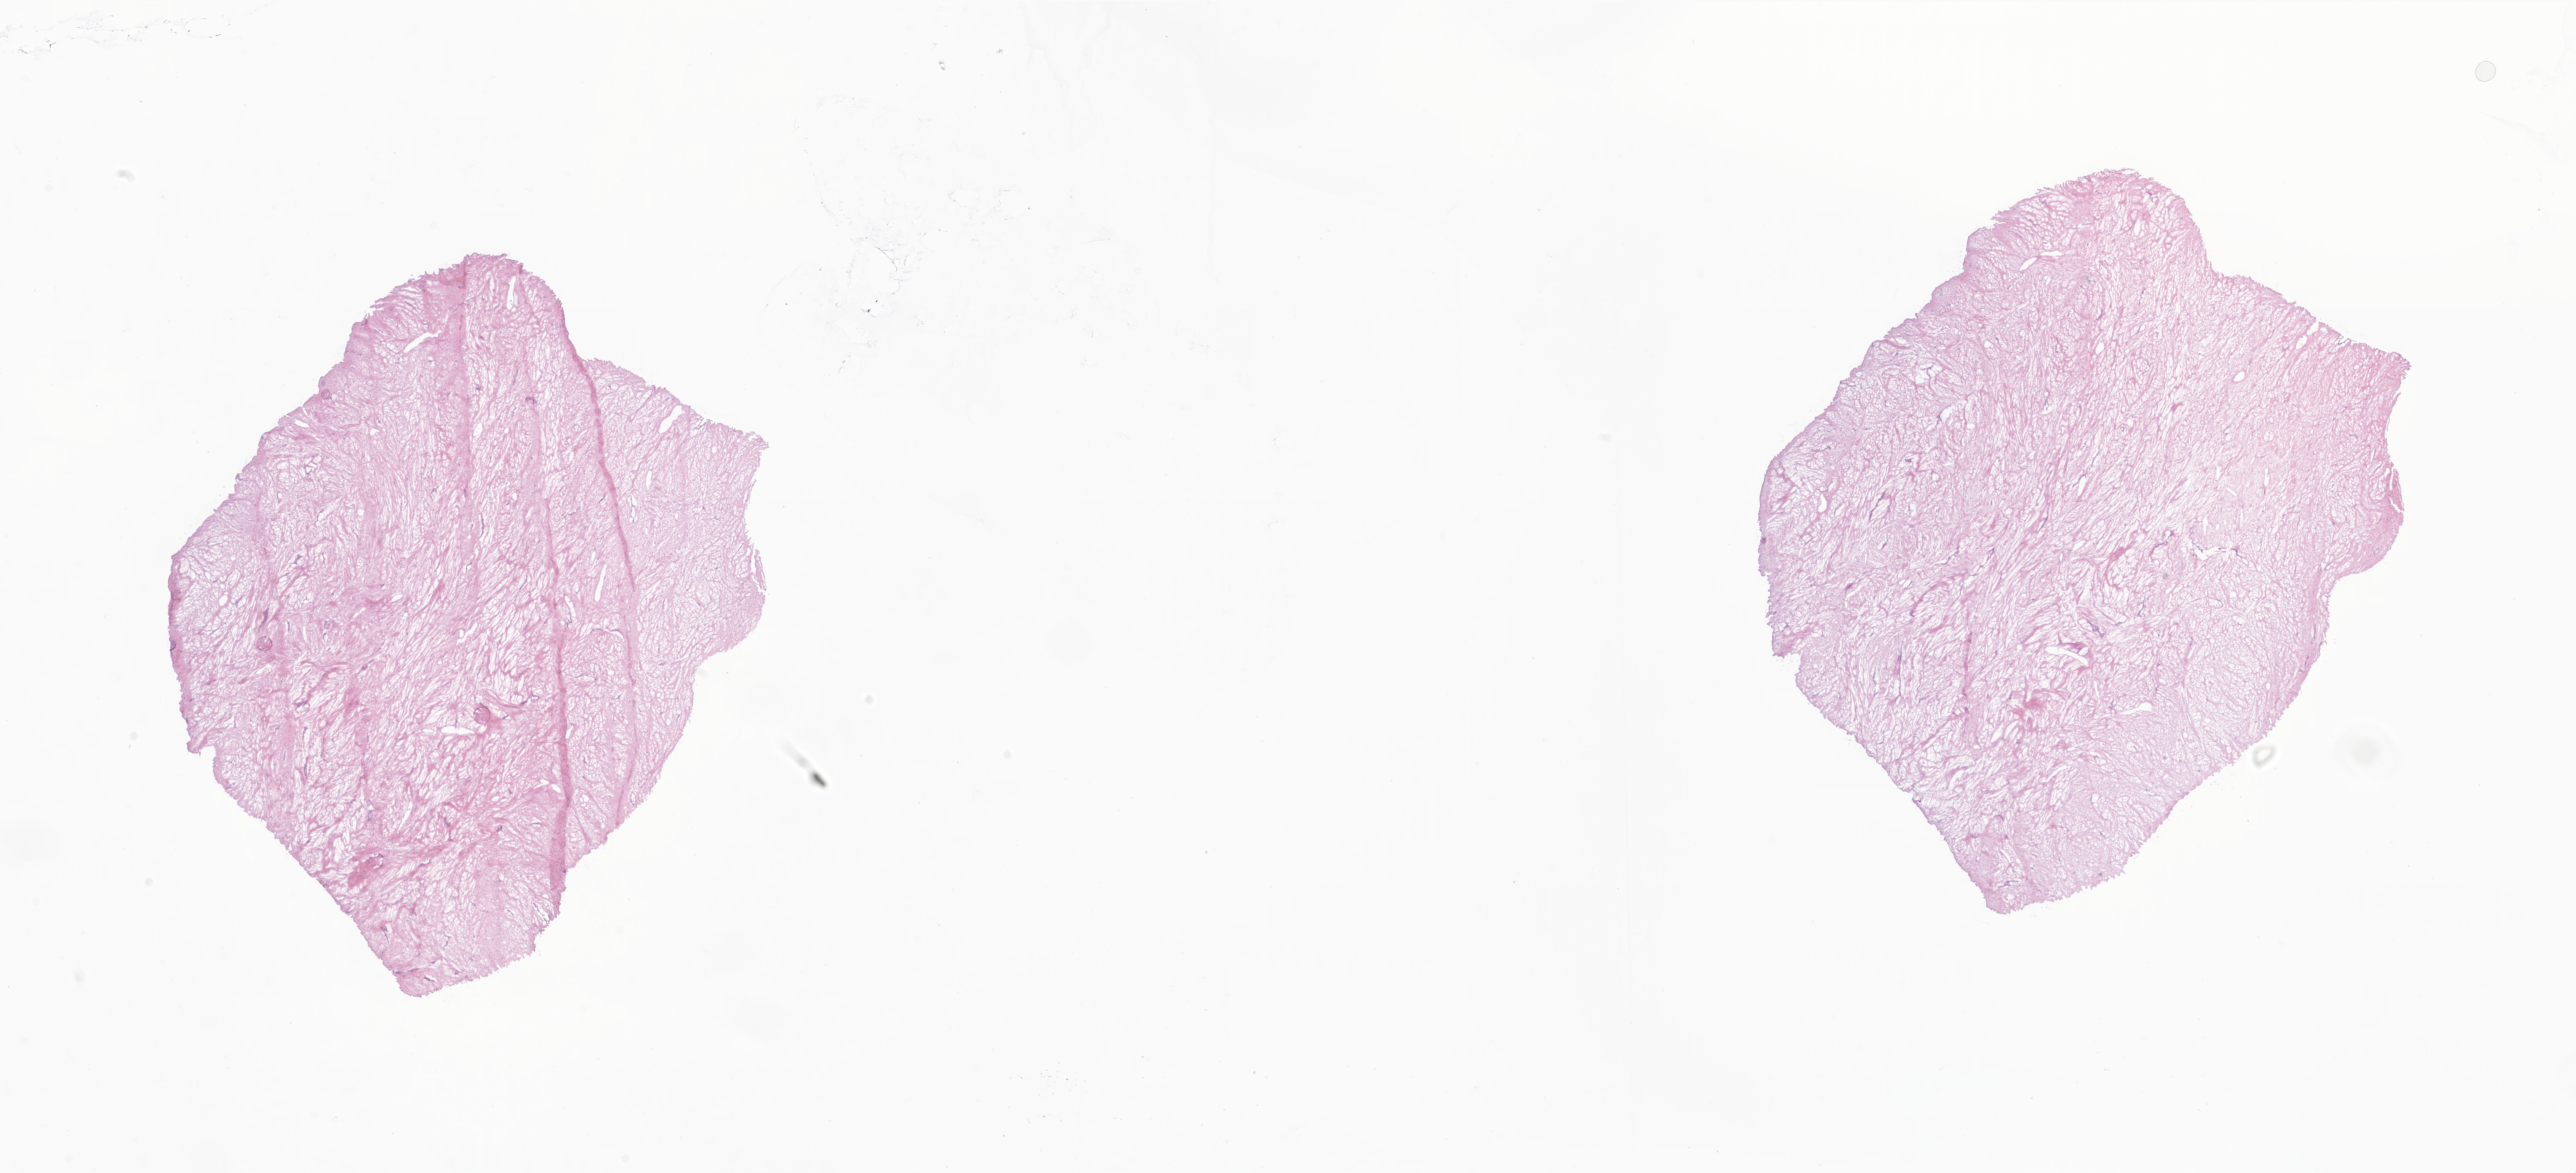
Digitized H&E-stained section of tumor tissue from the head and neck, low-resolution overview of the scanned area, about 28.6 x 13.0 mm, frozen section (OCT-embedded). Patient: female, age 78 months (6 years 6 months).
Diagnosis: Myxofibrosarcoma. Tissue or organ of origin (case record): head, face or neck.